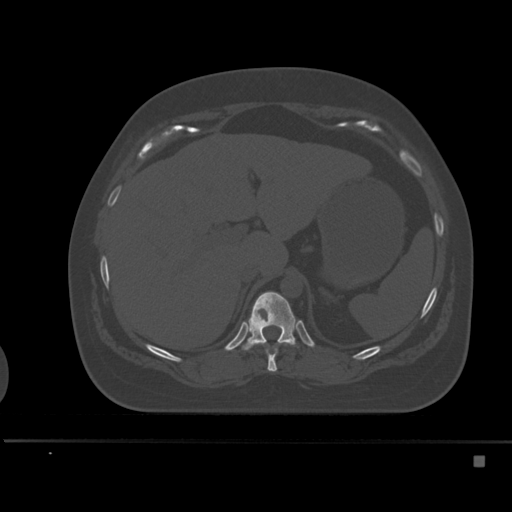
CT including the spine, one axial slice. Position 237 of 495 along the scan axis. Bone window (W 1800 / L 400 HU). 1.5 mm slice thickness. 512 × 512 image matrix, field of view 404 × 404 mm. Female patient, age 33 years. From the clinical record (not read from this slice): primary cancer: breast; vertebrae with lytic lesions (as recorded): T1.
Annotated regions visible in this slice (semi-automatically segmented with operator editing):
- T10 vertebra: bounding box (x1, y1, x2, y2) in pixels: (261, 343, 291, 372)
- T11 vertebra: (241, 291, 299, 350)